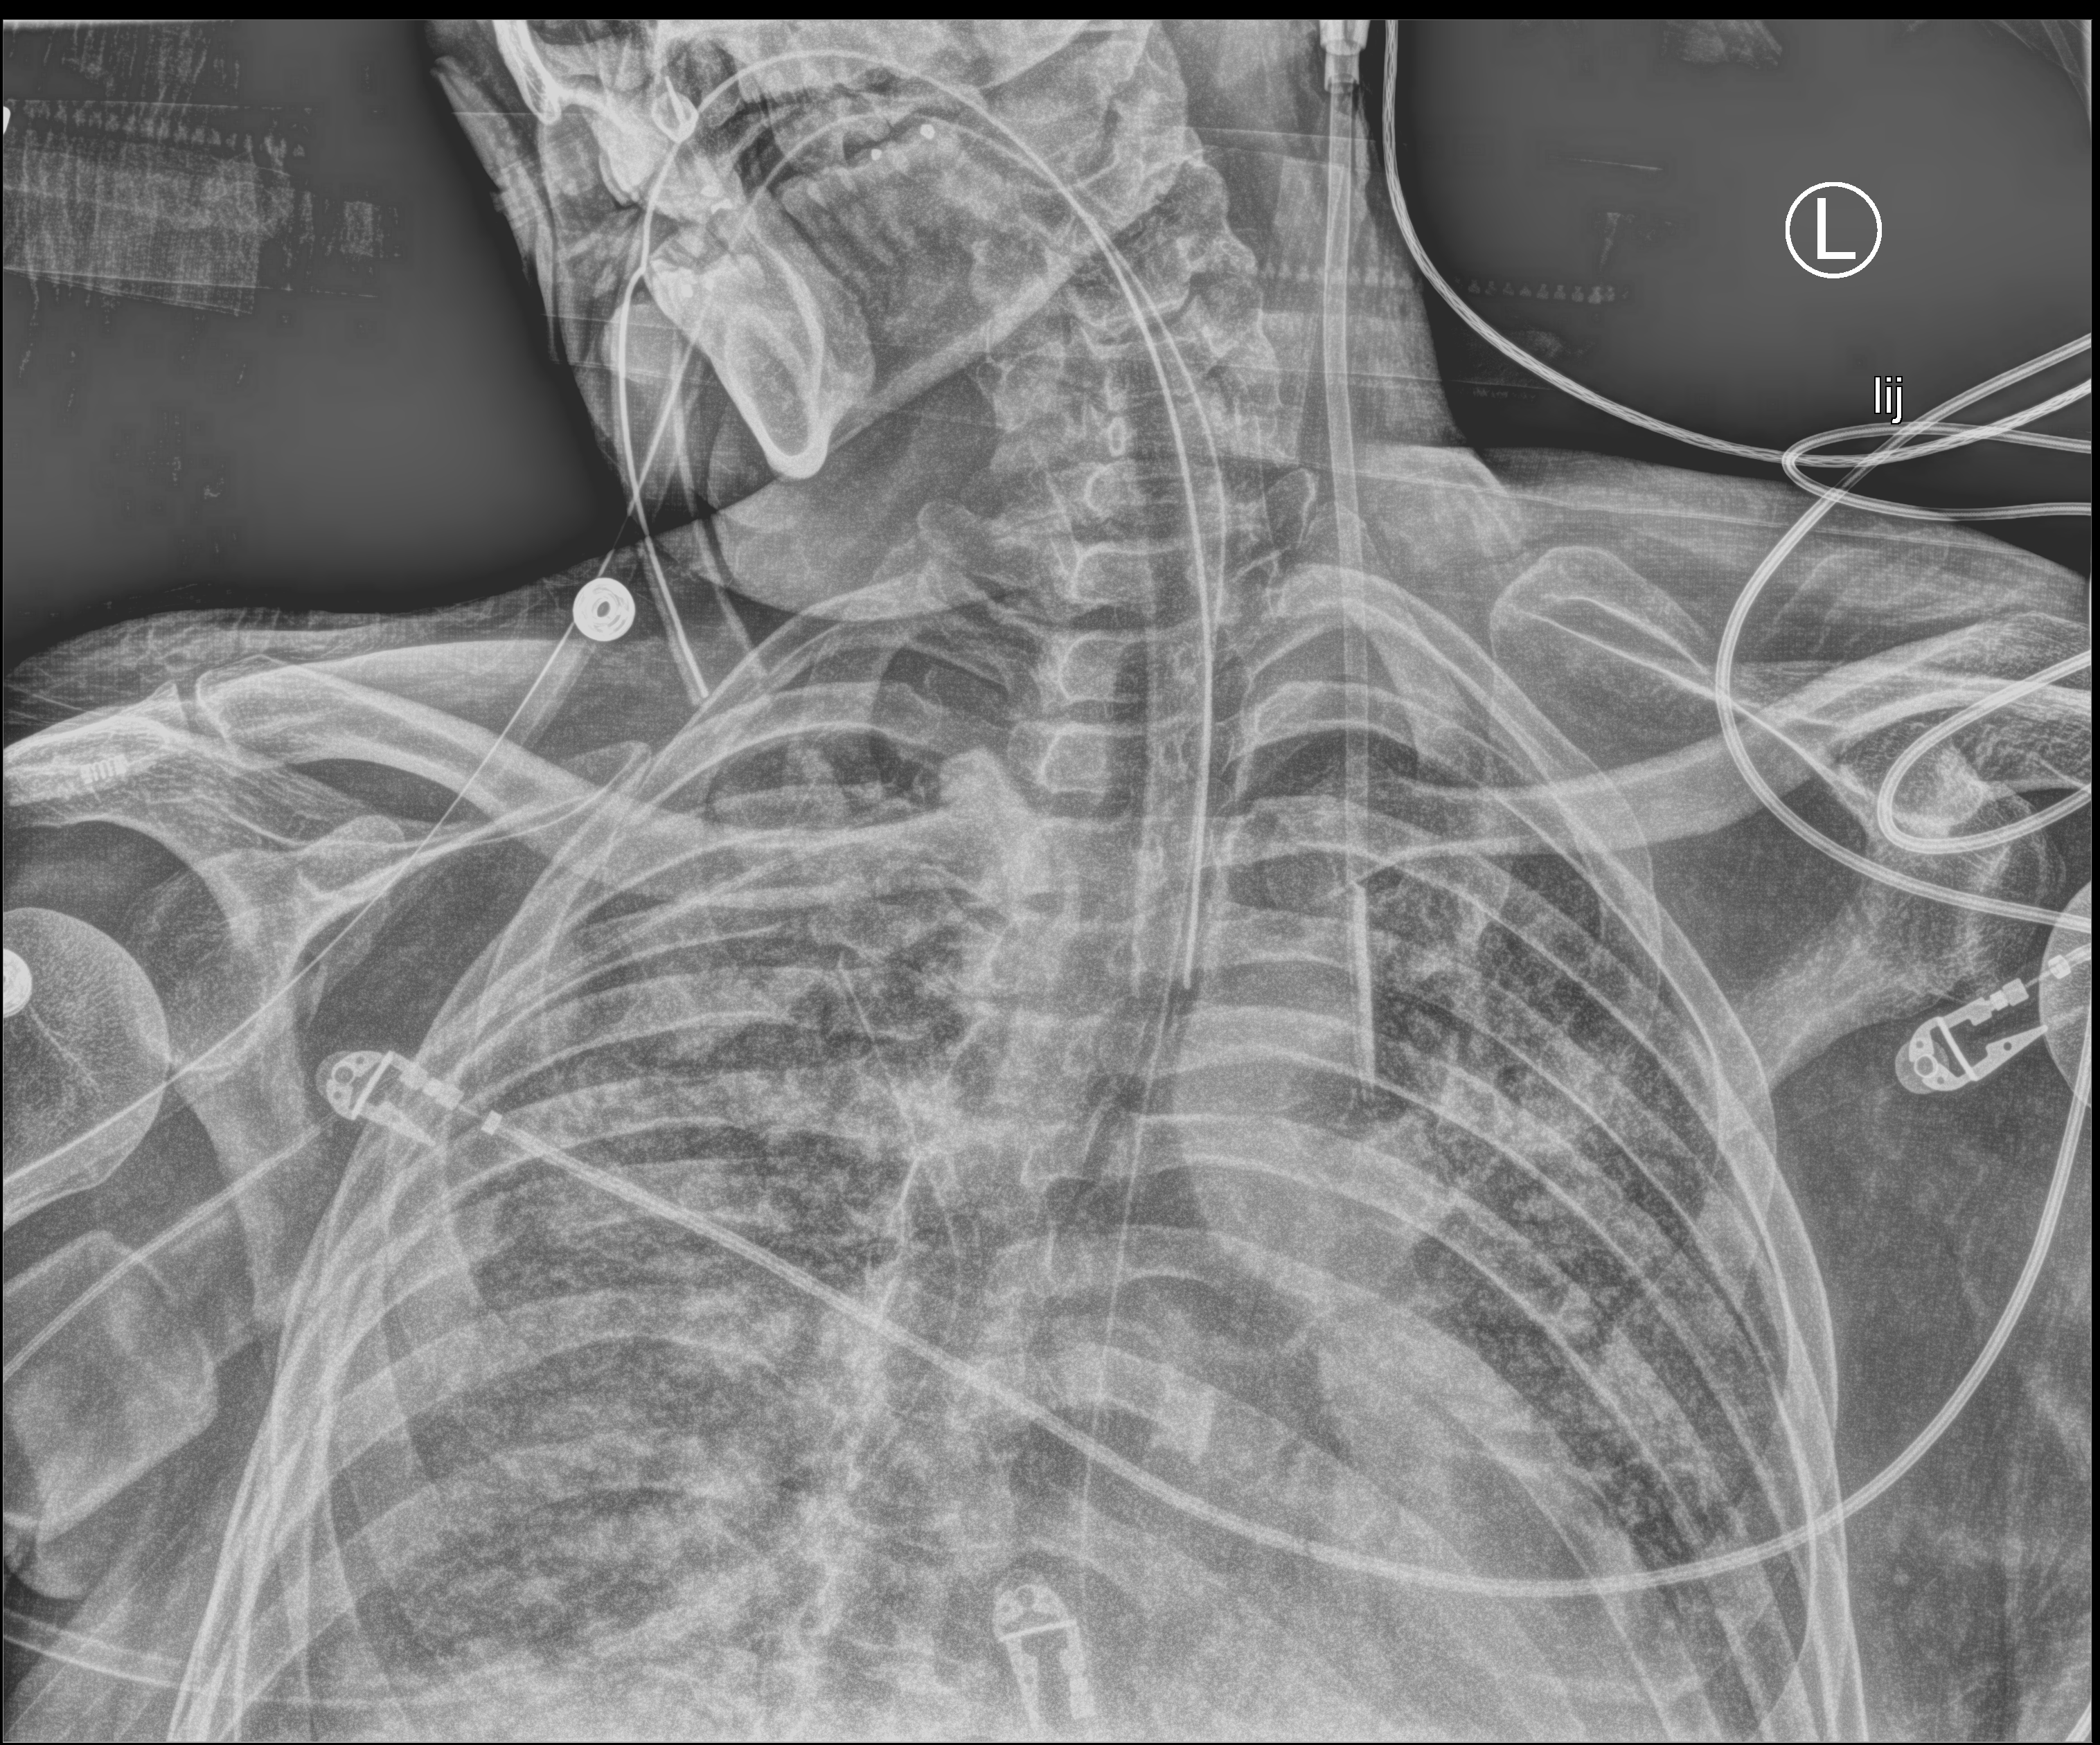
Chest X-ray (portable). Male patient hospitalised with COVID-19, age 18–59 years.
From the hospital-stay record, not from the radiograph (when in the stay this image was taken is not recorded):
- admitted to intensive care during this hospital stay: yes
- chronic kidney disease (admission record): no